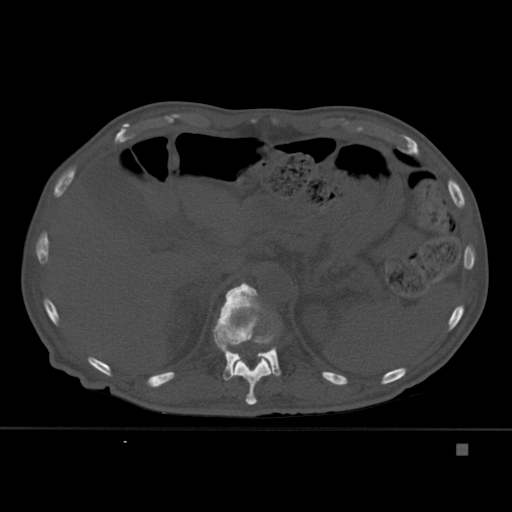
CT including the spine, one axial slice; slice 209 of 451 in the series (ordered by position); bone window (W 1800 / L 400 HU); 1.5 mm slice thickness; 512 × 512 image matrix, field of view 378 × 378 mm. Patient: male, 75 years. From the clinical record (not read from this slice): primary cancer: prostate.
Annotated regions visible in this slice (semi-automatic segmentation, software-assisted and operator-edited):
- T11 vertebra: bounding box (x1, y1, x2, y2) in pixels: (233, 310, 279, 405)
- T12 vertebra: (212, 283, 282, 381)